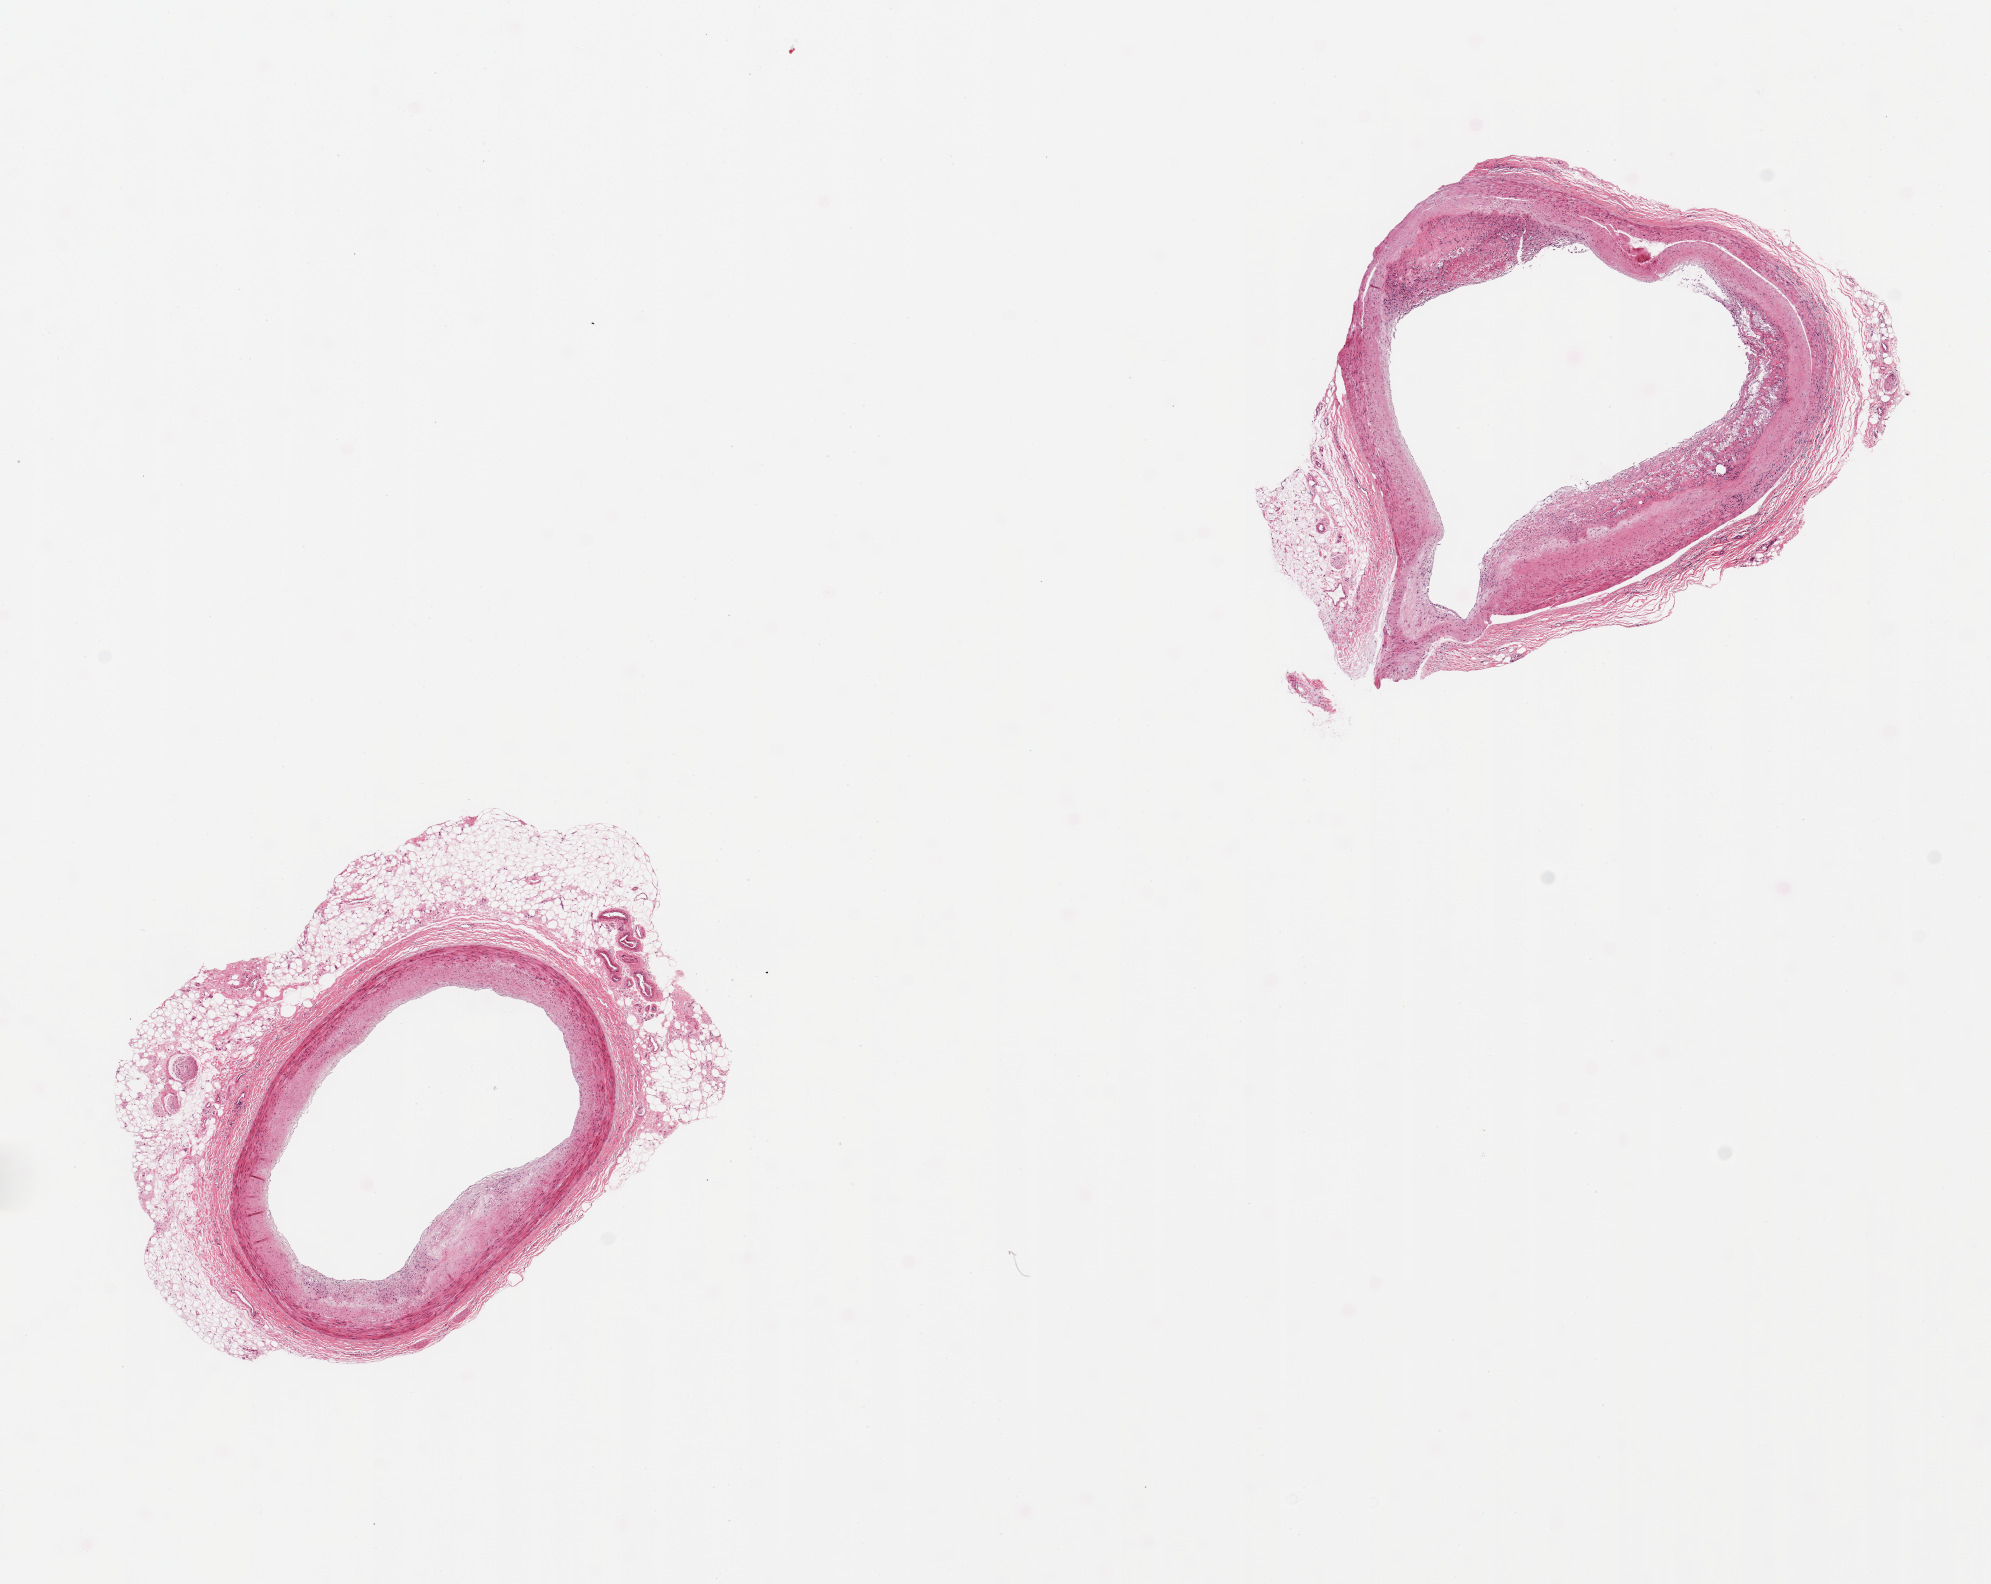
Digitized hematoxylin and eosin (H&E)-stained section, brightfield, a low-resolution overview of the entire scanned area, about 15.8 x 12.5 mm; PAXgene-fixed paraffin-embedded (PFPE) section; target tissue: coronary artery; donor tissue sample. Donor sex: female.
Review note (as recorded): 2 pieces, ~20% occlusive atherosis, rim of adherent fat ~0.5mm.